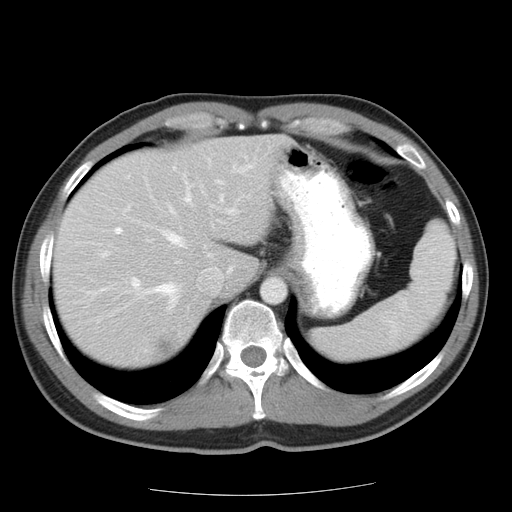
Contrast-enhanced abdominal CT, one axial slice; position 16 of 22 along the scan axis; intravenous contrast given; soft-tissue window (W 400 / L 40 HU); 512 × 512 image matrix, field of view 359 × 359 mm. Male patient, age 41 years. Case-level facts recorded for this patient, not image findings: diagnosis: colorectal cancer liver metastases, imaged before liver resection; multiple liver metastases: no; largest metastasis: 2.7 cm; disease in both lobes: no.
Structures marked on this image (expert manual segmentation):
- hepatic veins: box from (x=146, y=197) to (x=223, y=308) px
- liver: (x=55, y=136)–(x=279, y=365)
- planned liver remnant (the part of the liver to remain after resection): (x=55, y=136)–(x=279, y=335)
- portal vein (with intrahepatic branches): (x=114, y=166)–(x=250, y=297)
- liver metastasis: (x=151, y=333)–(x=180, y=358)